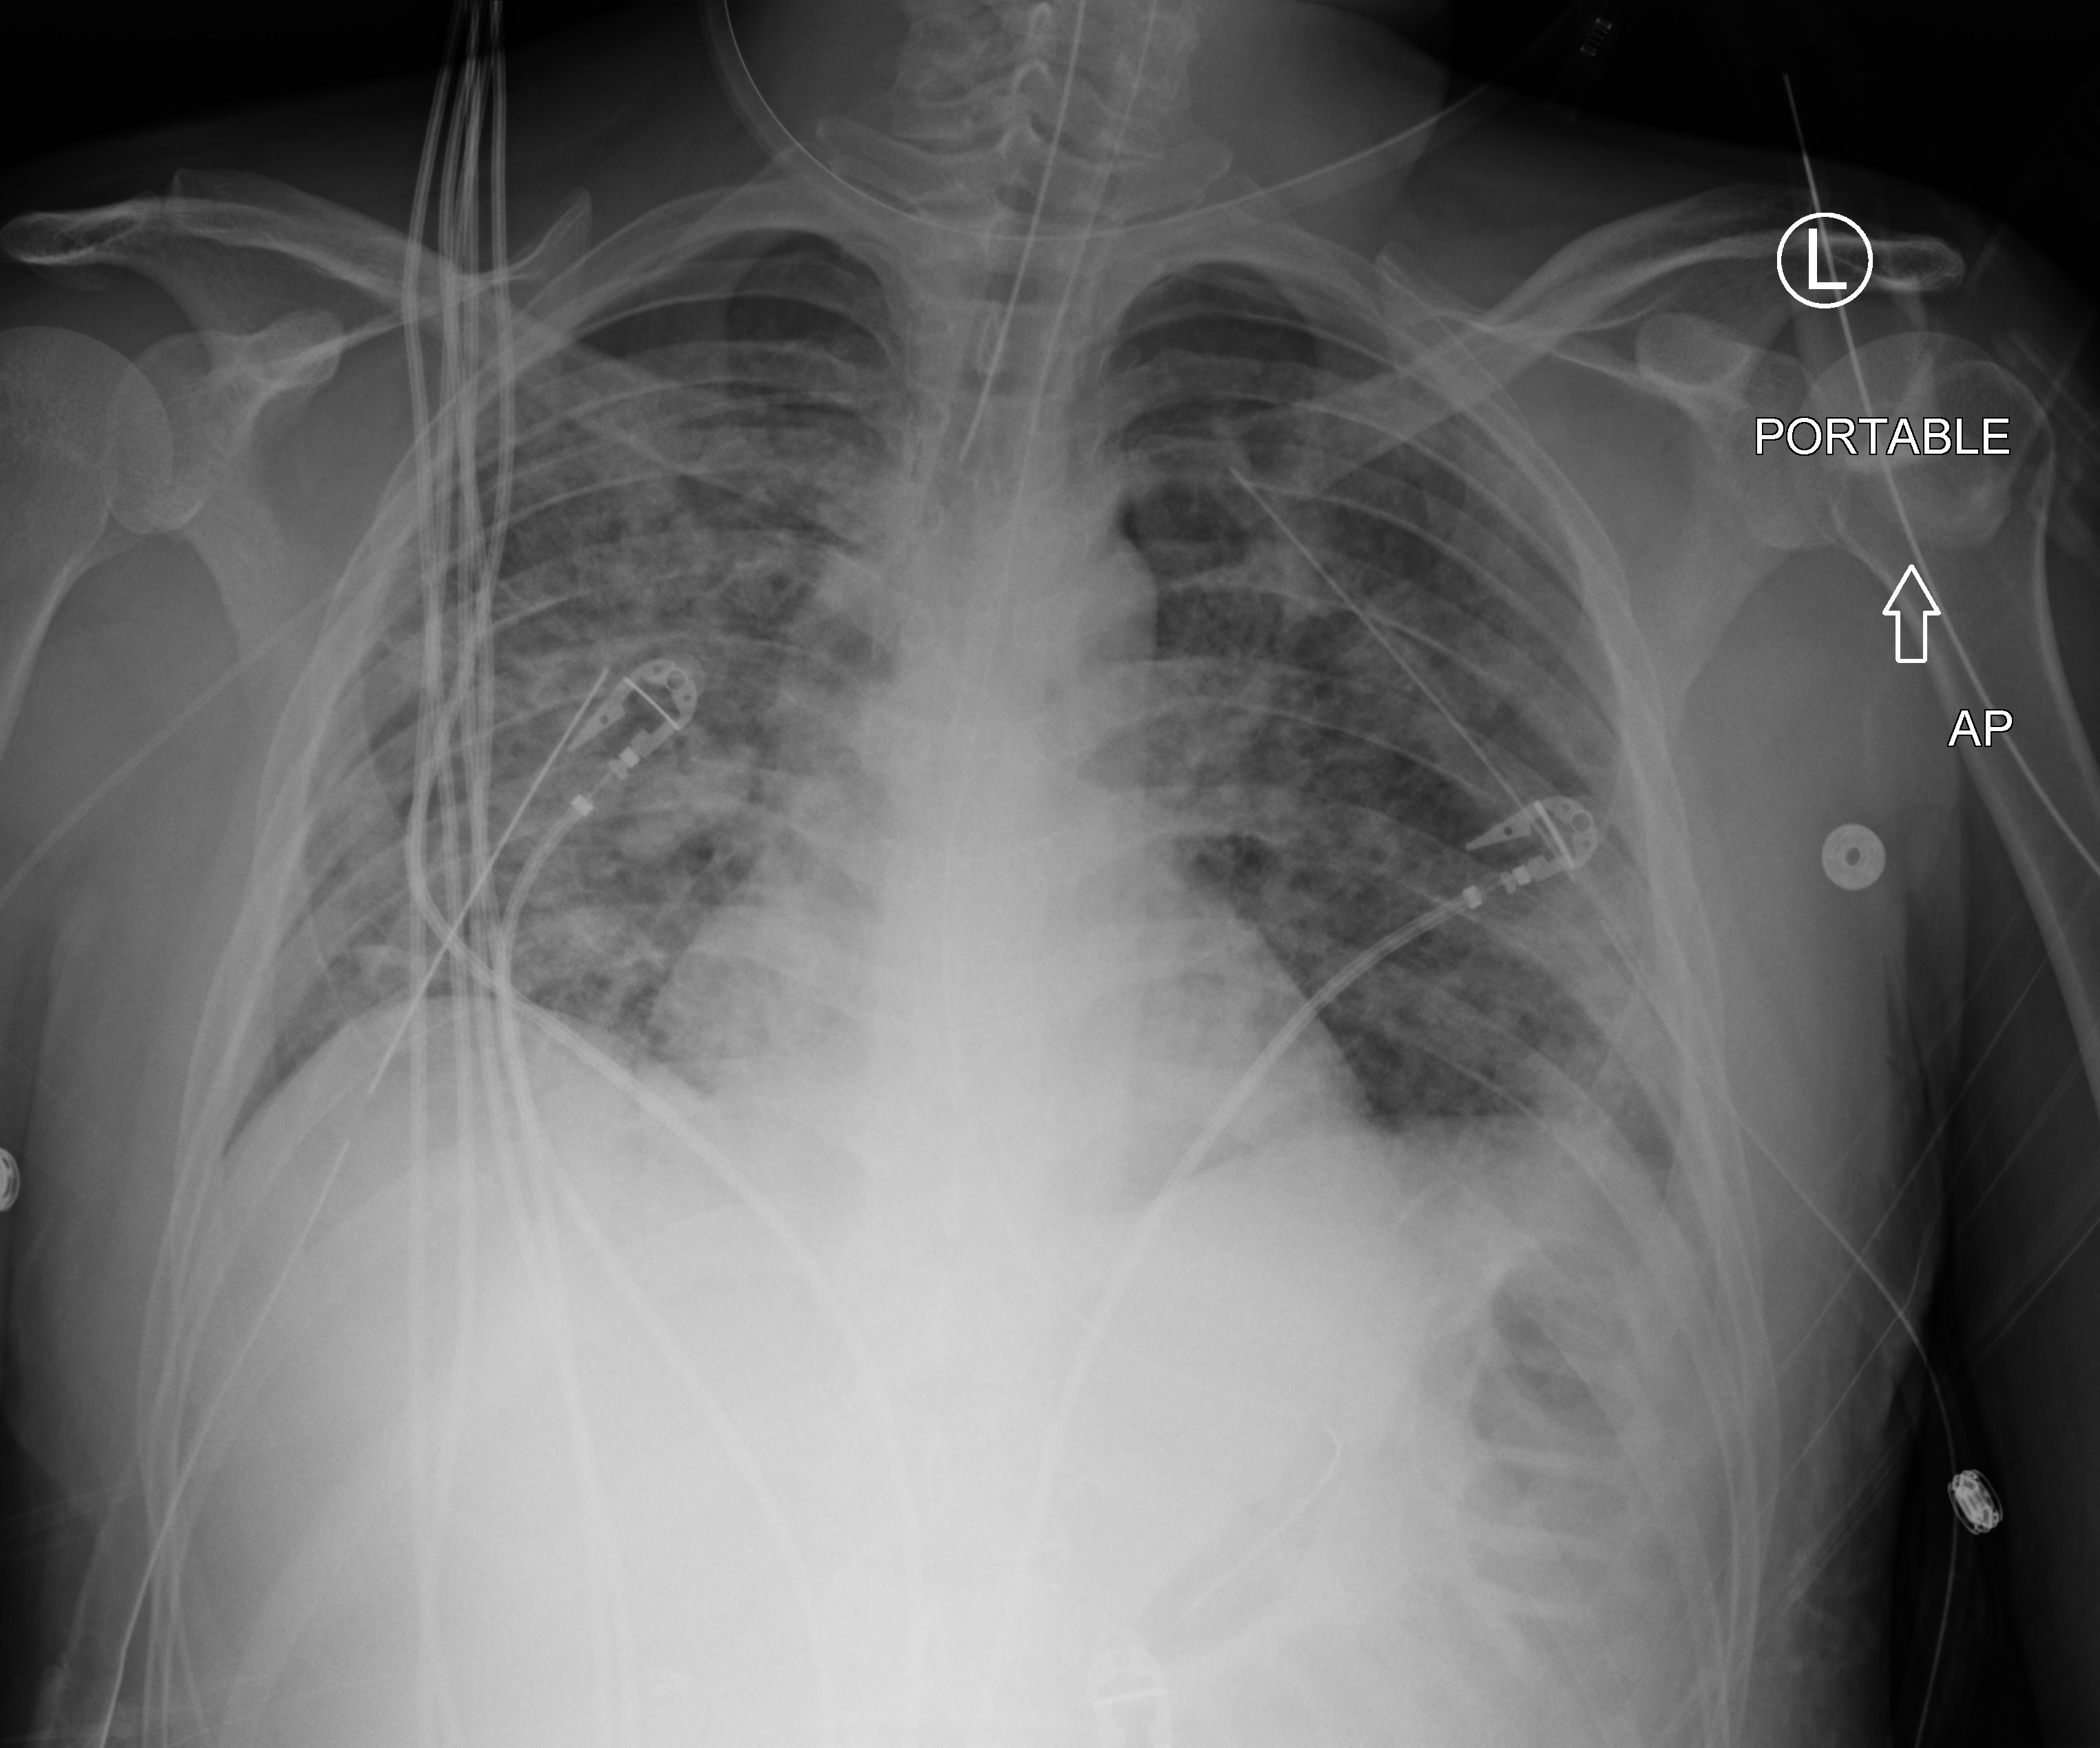
Bedside chest radiograph (computed radiography), anteroposterior (AP) projection. Male patient hospitalised with COVID-19, age 18–59 years.
Admission-level facts for this patient (not findings on this image; timing relative to this image not recorded):
- other chronic lung disease (admission record): no